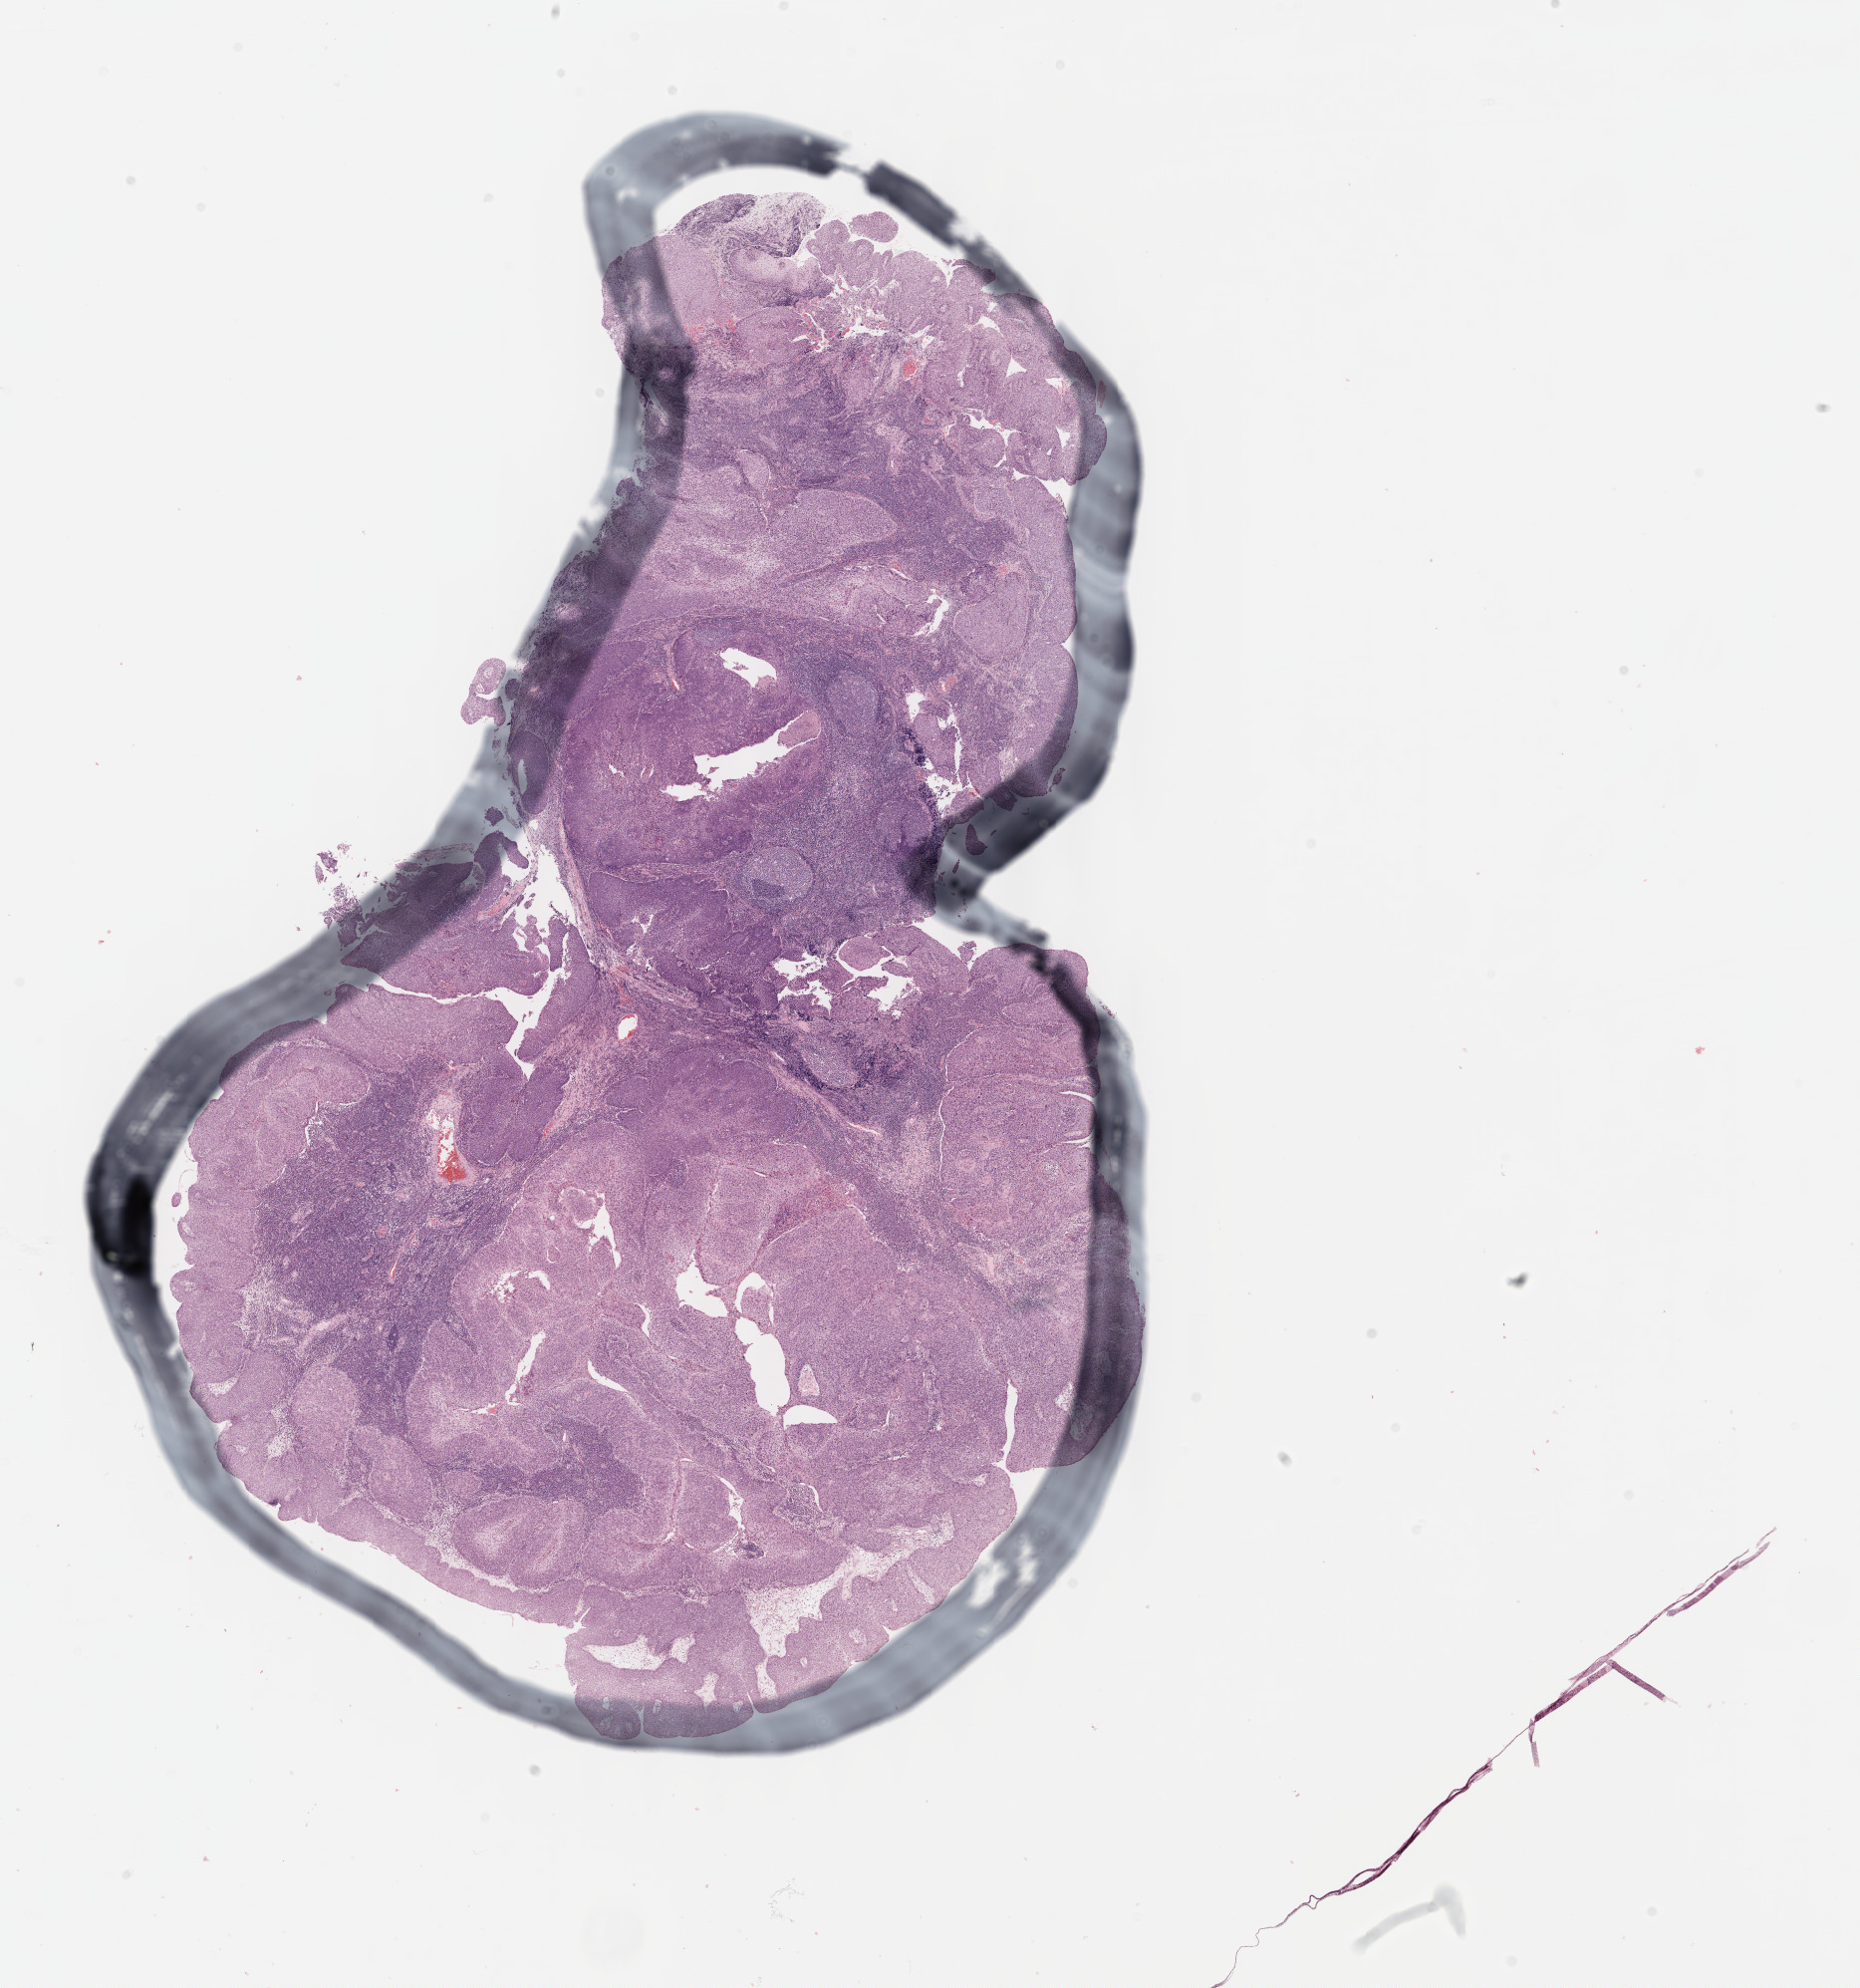
Whole-slide histology image, H&E — low-resolution overview of the scanned area, about 15.1 x 16.1 mm, FFPE section, head and neck, primary tumour sample. Male patient; age at initial diagnosis 47 years. Histologic grade: G4 (undifferentiated).
Laterality: right. Pathologic diagnosis: Squamous cell carcinoma, NOS (base of tongue, NOS).